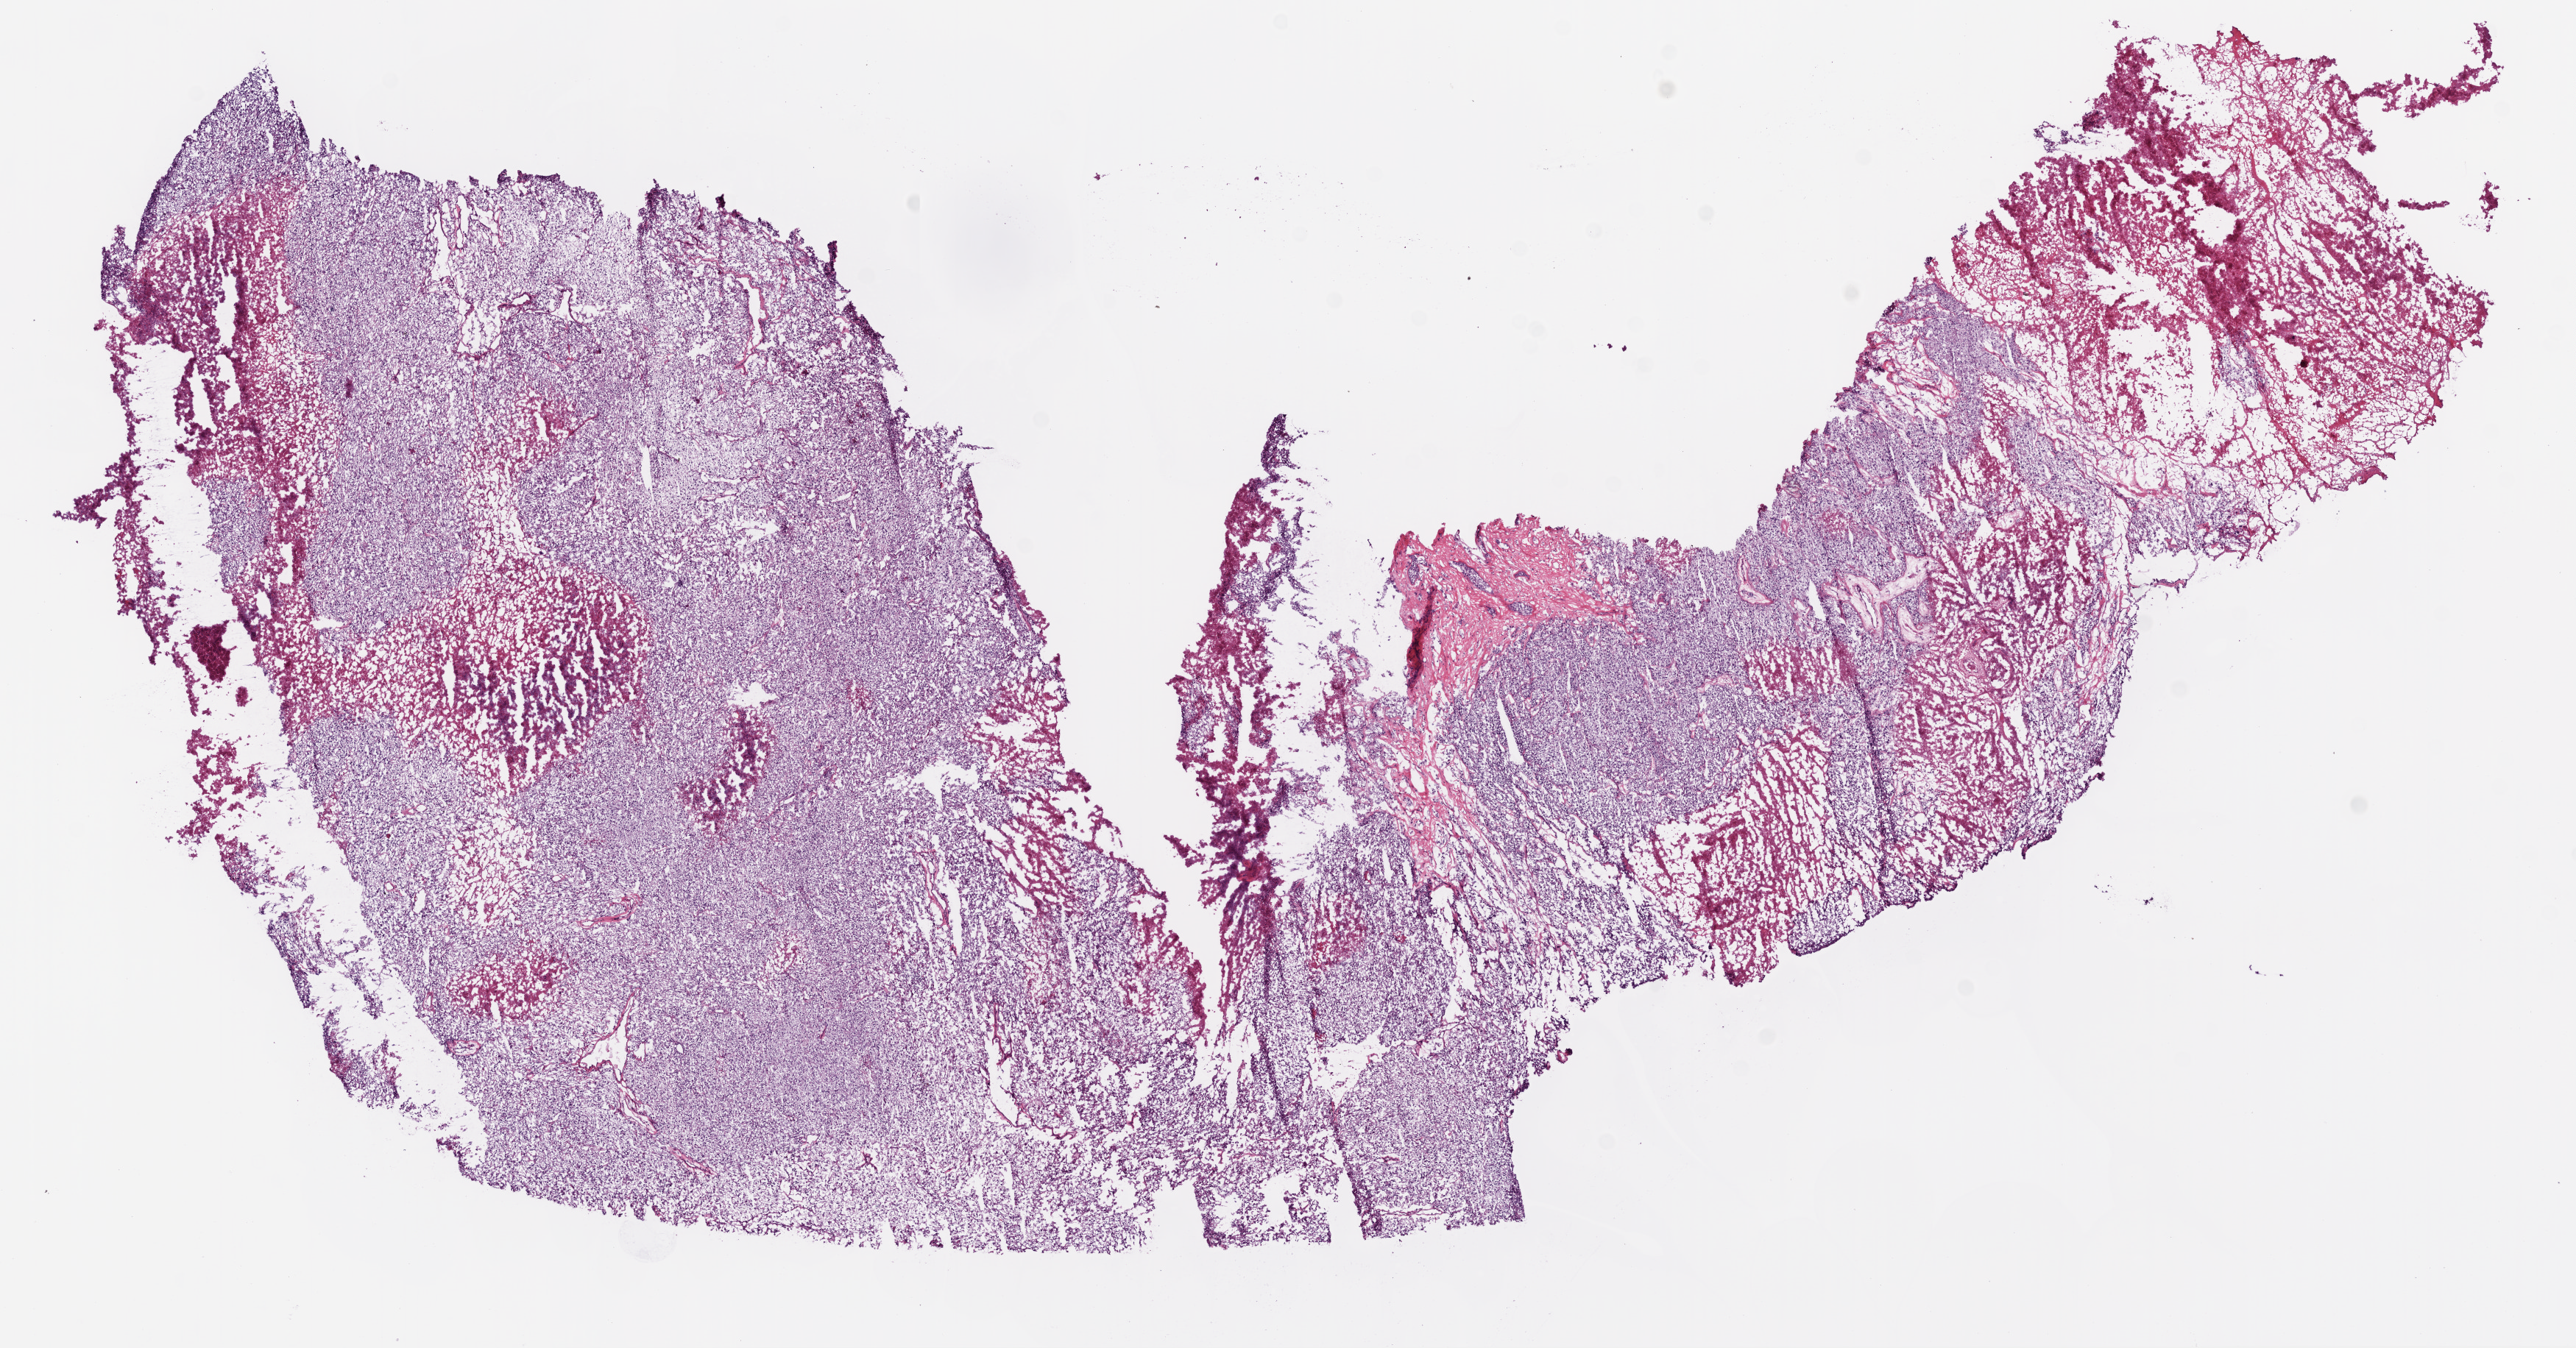
H&E-stained whole-slide image — whole scanned area (about 14.0 x 7.4 mm) shown as a low-resolution overview. Frozen section. Sample: primary tumour, kidney. Male patient; age at initial diagnosis 68 years. Histologic grade: G3 (poorly differentiated). Slide review estimates, as recorded: tumour cells 70%, tumour nuclei 80%, normal cells 0%, stromal cells 10%, necrosis 20%. Inflammatory infiltration, as recorded: lymphocyte infiltration 15%, monocyte infiltration 1%, neutrophil infiltration 0%.
Histologic diagnosis: Clear cell adenocarcinoma, NOS. AJCC pathologic stage: I. Laterality: left.